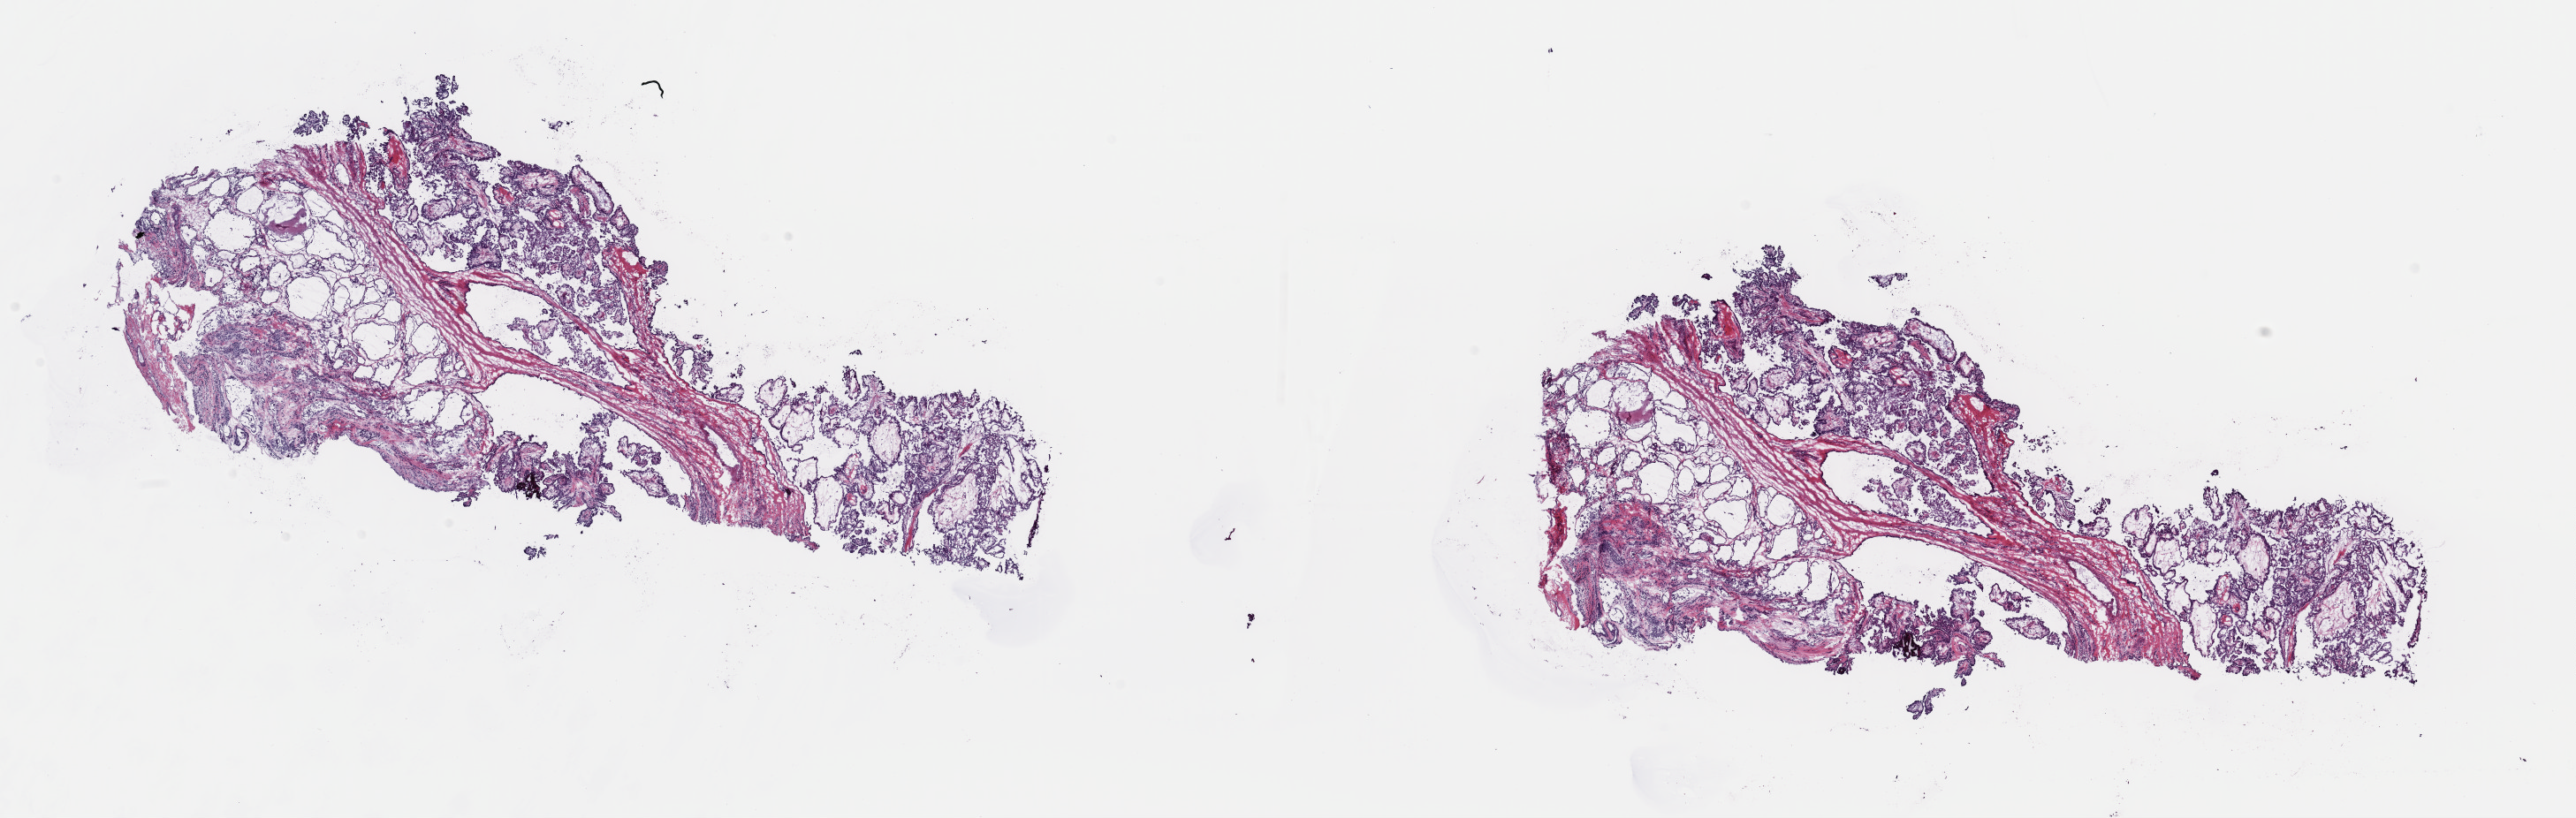
Digitized H&E tissue section (whole slide) — whole scanned area (about 23.0 x 7.3 mm, from a 40x scan) shown as a low-resolution overview, frozen section, sample: primary tumour, thyroid. Patient: female, age at initial diagnosis 31 years. Slide review estimates, as recorded: tumour cells 50%, tumour nuclei 60%.
Histologic diagnosis: Papillary adenocarcinoma, NOS (thyroid gland).